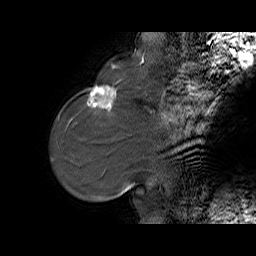
Breast MRI (dynamic contrast-enhanced), one sagittal slice; dynamic contrast-enhanced series, time point 2 of 6 at this slice position (early post-contrast); 1.5 T; TE 5.7 ms, TR 32.9 ms; 256 × 256 image matrix, field of view 230 × 230 mm. Female patient. From the clinical record (not read from this slice): setting: breast cancer imaged before/during neoadjuvant chemotherapy; receptor status: HER2-positive.
Outlined on this slice (semi-automatic segmentation, software-assisted and operator-edited):
- analysis volume of interest (the breast-tissue region the enhancement analysis was run in; not a lesion): box from (x=76, y=77) to (x=125, y=128) px
- tumour enhancement mask (voxels above the 100 % enhancement threshold inside the analysis volume of interest): (x=87, y=86)–(x=116, y=109)